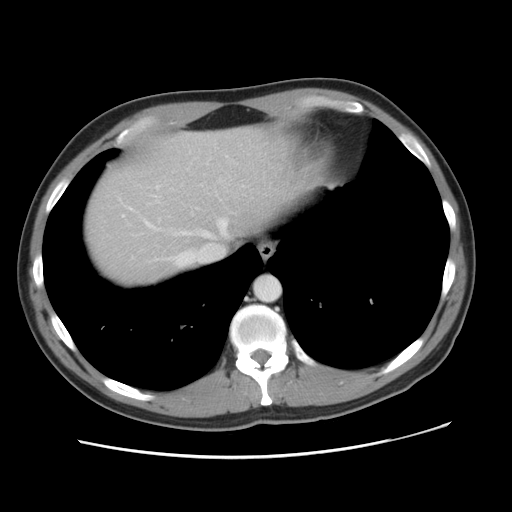
Contrast-enhanced abdominal CT, one axial slice; slice 42 of 49 in the series (ordered by position); reconstruction kernel STANDARD; soft-tissue window (W 400 / L 40 HU); 5 mm slice thickness; 512 × 512 image matrix, field of view 363 × 363 mm. Male patient, age 41 years. Case-level facts recorded for this patient, not image findings: diagnosis: colorectal cancer liver metastases, imaged before liver resection; multiple liver metastases: yes; largest metastasis: 0.7 cm; chemotherapy before resection: yes.
Outlined on this slice (expert manual segmentation):
- hepatic veins: bounding box [x1, y1, x2, y2] px = [125, 199, 228, 266]
- liver: [83, 129, 291, 287]
- planned liver remnant (the part of the liver to remain after resection): [113, 129, 290, 249]
- portal vein (with intrahepatic branches): [156, 186, 159, 188]